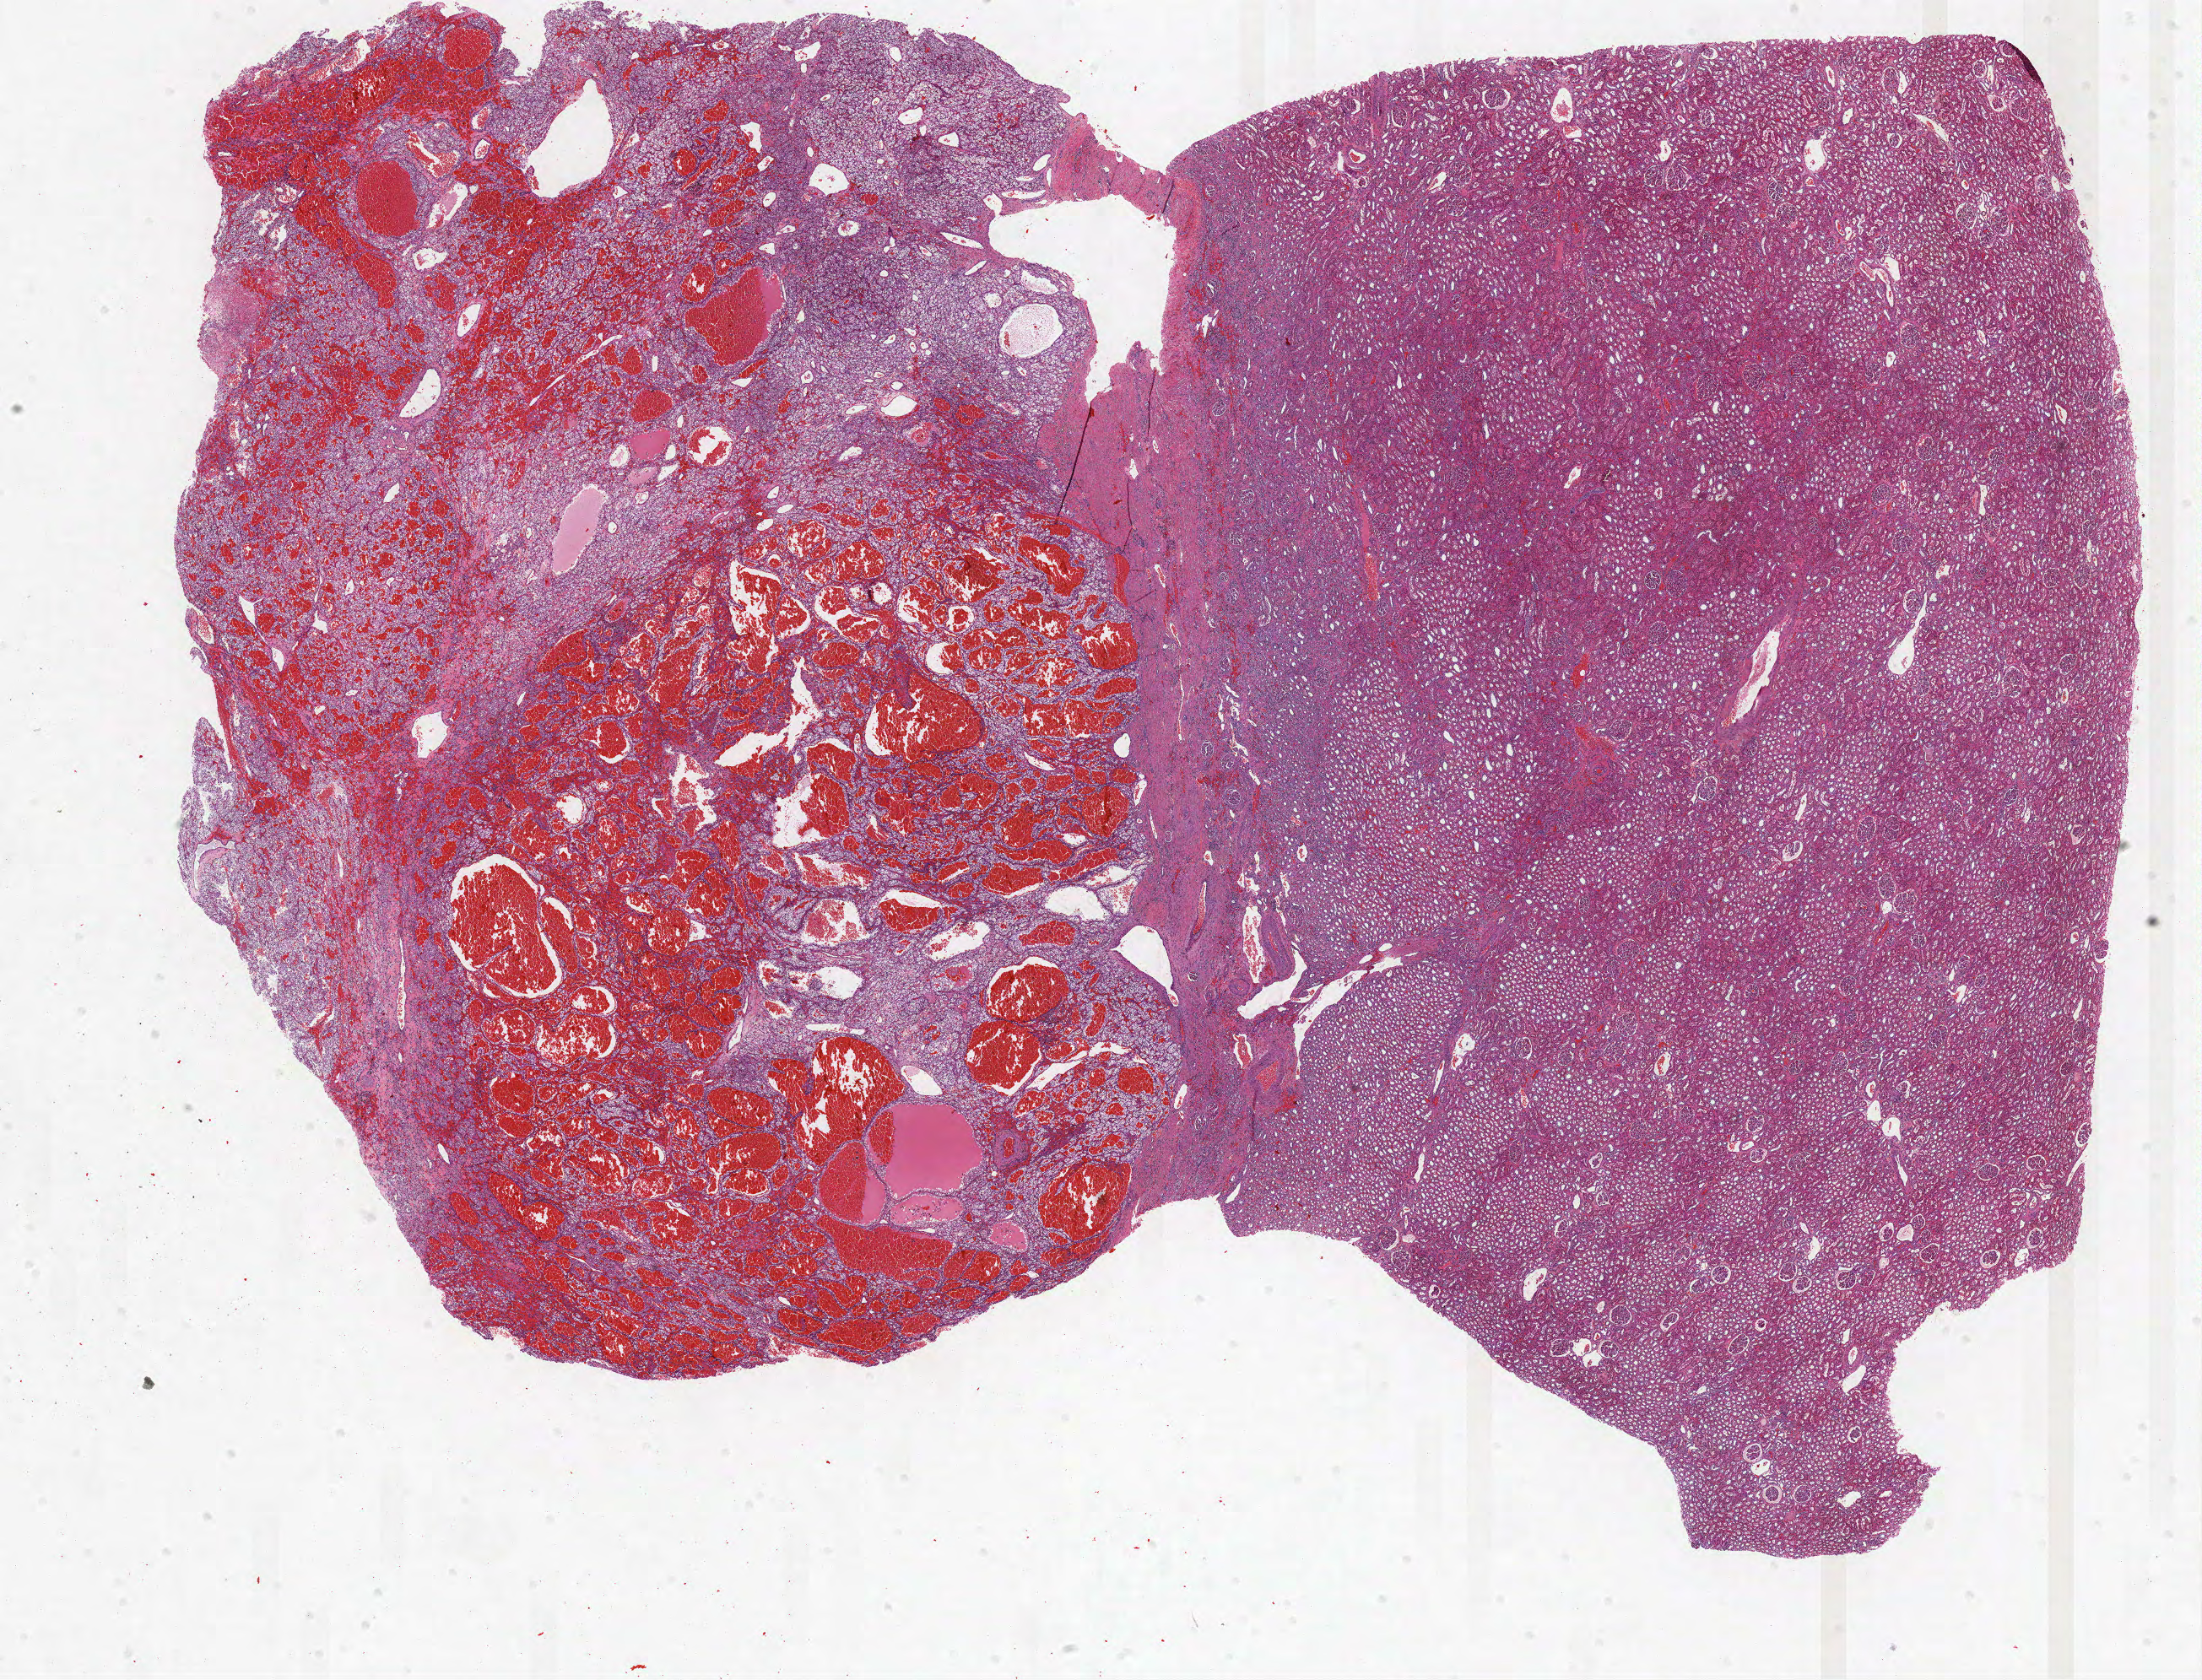
Digitized Hematoxylin and eosin (H&E) stained tissue section (whole slide) — whole scanned area (about 20.9 x 15.9 mm, from a 40x scan) shown as a low-resolution overview. Formalin-fixed paraffin-embedded (FFPE) diagnostic section. Kidney, primary tumour sample. Male, age 49 years at initial diagnosis. Histologic grade: G3 (poorly differentiated).
Lymph nodes positive (case pathology): 0 of 3 examined. AJCC pathologic stage: II. TNM: T2 N0 M0. Histologic diagnosis: Clear cell adenocarcinoma, NOS.